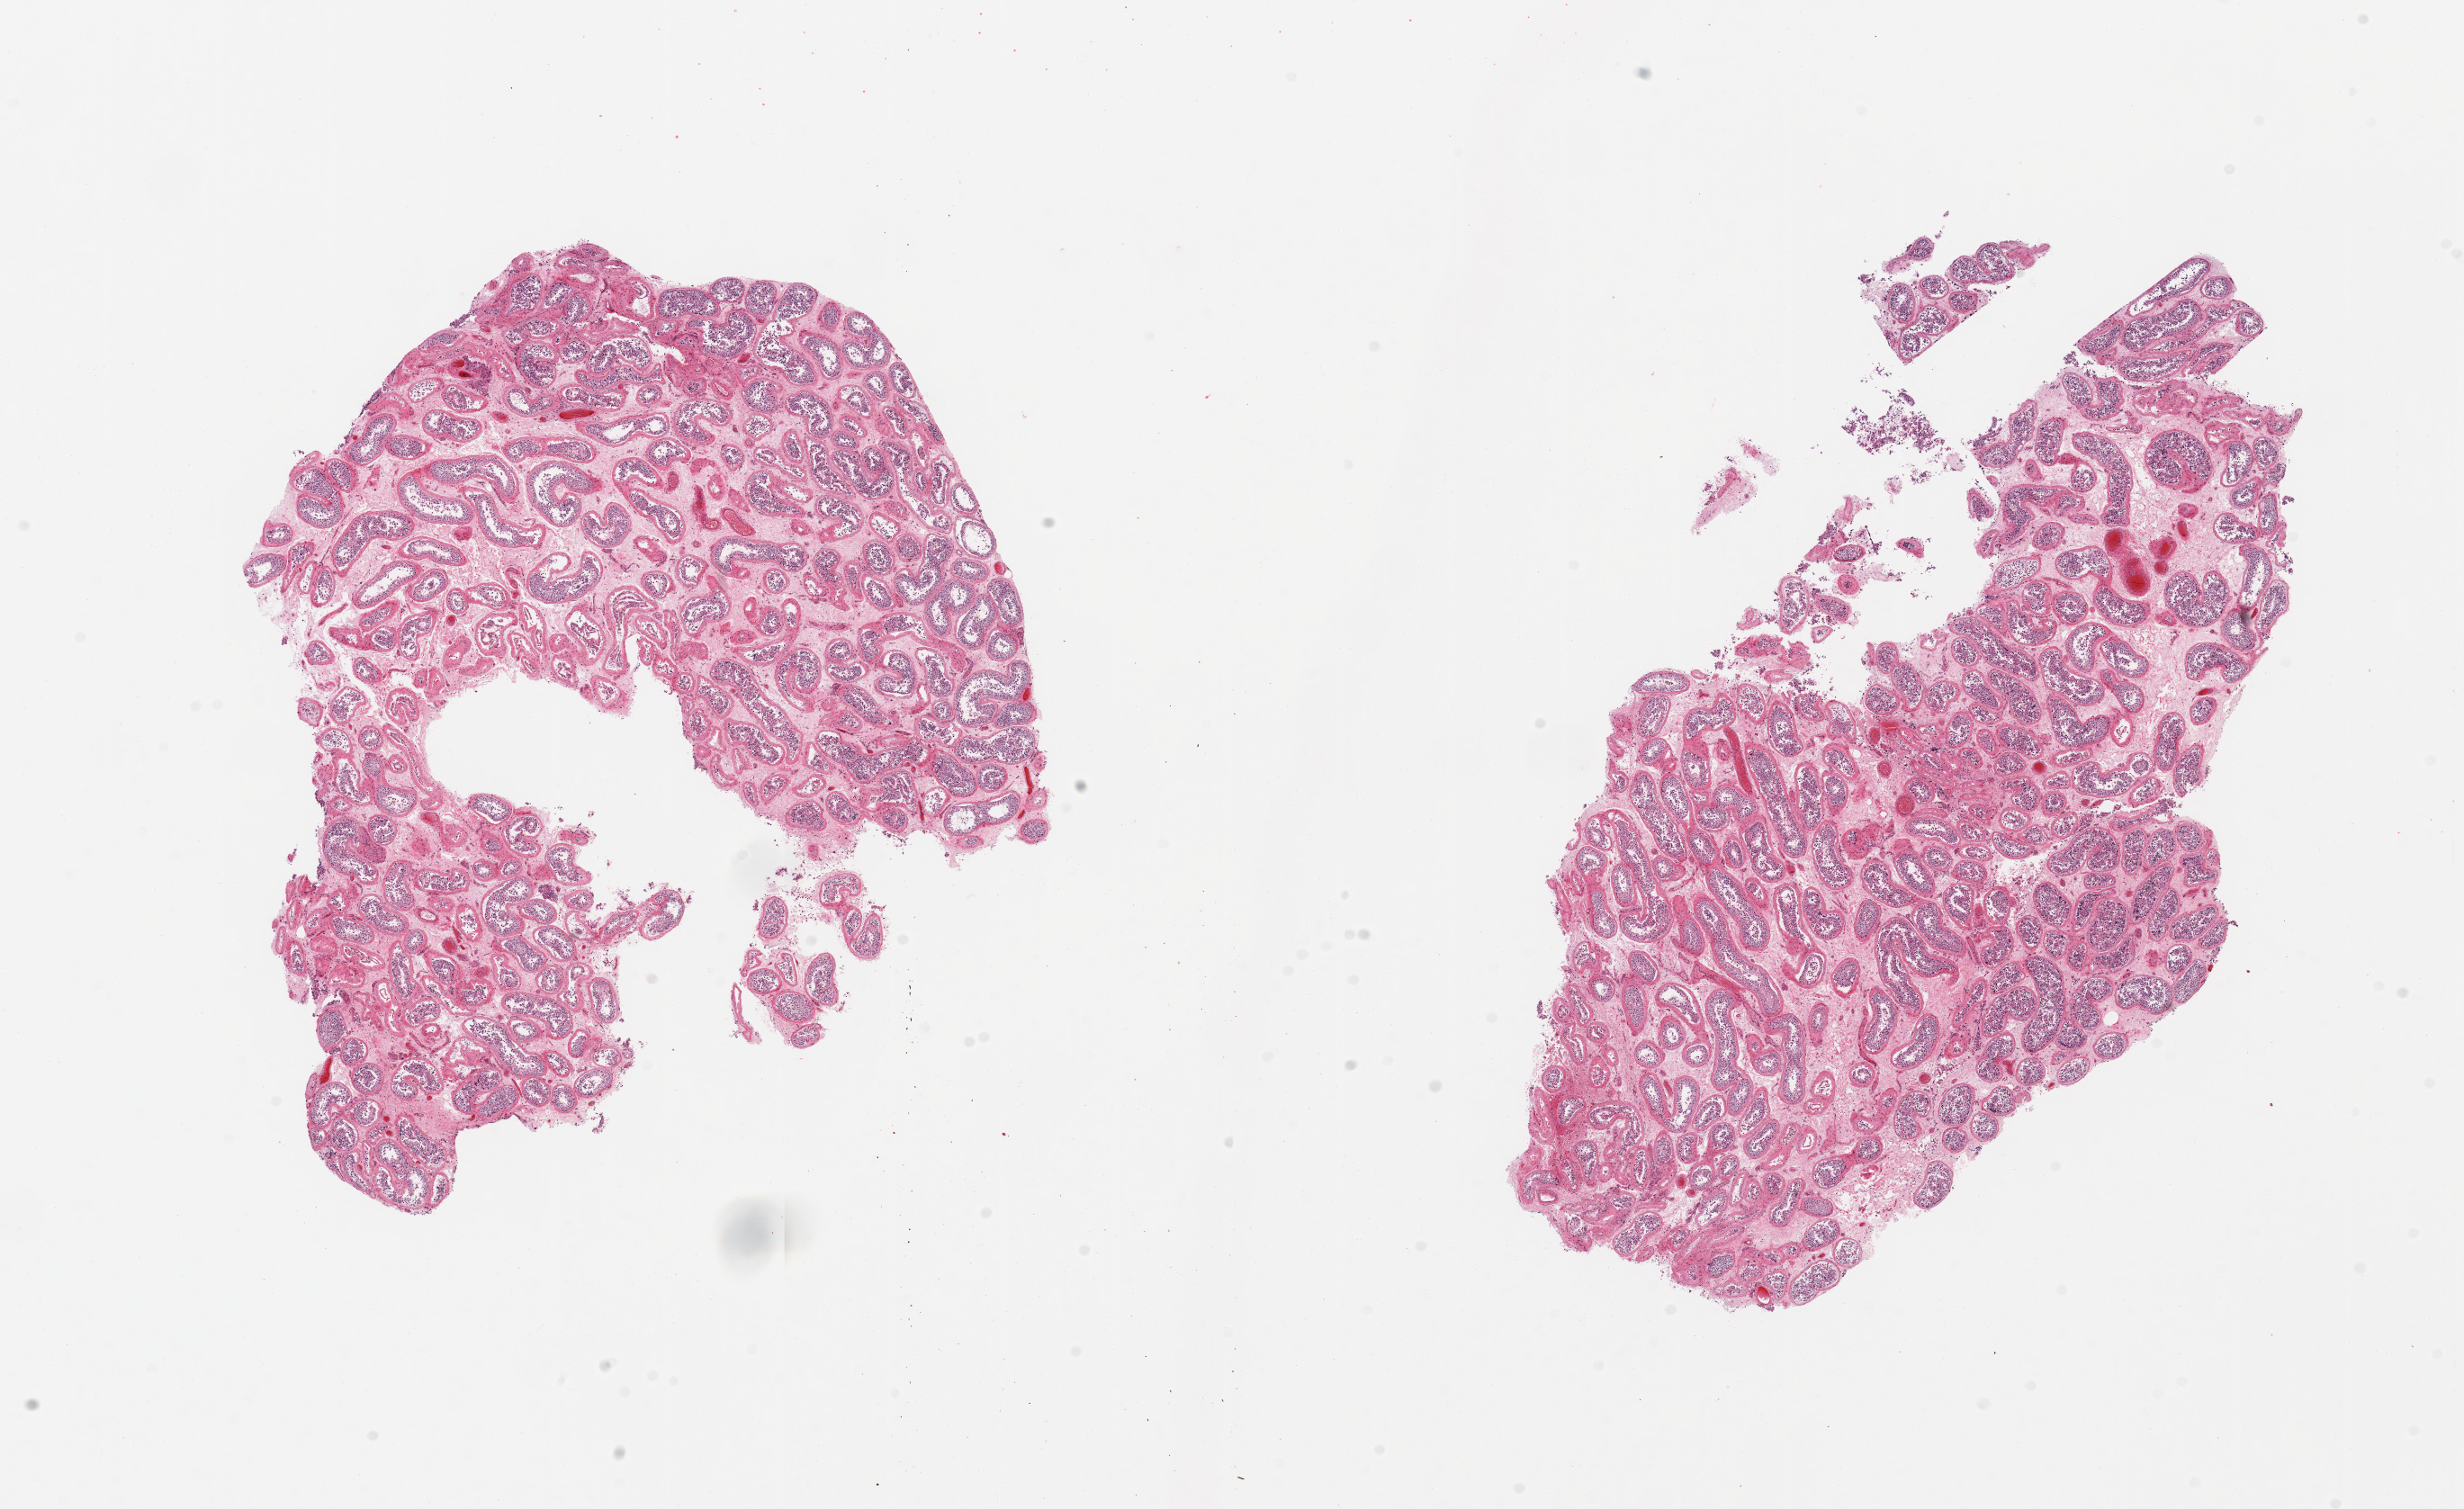
Whole-slide image, haematoxylin and eosin stain, shown as a low-resolution overview of the whole scanned area (about 21.7 x 13.3 mm, from a 20x scan), PAXgene-fixed, paraffin-embedded tissue, target tissue: testis, tissue donor sample.
Reviewer comment on this tissue sample: 2 pieces, prominent interstitial fibrosis; spermatogenesis appears reduced.